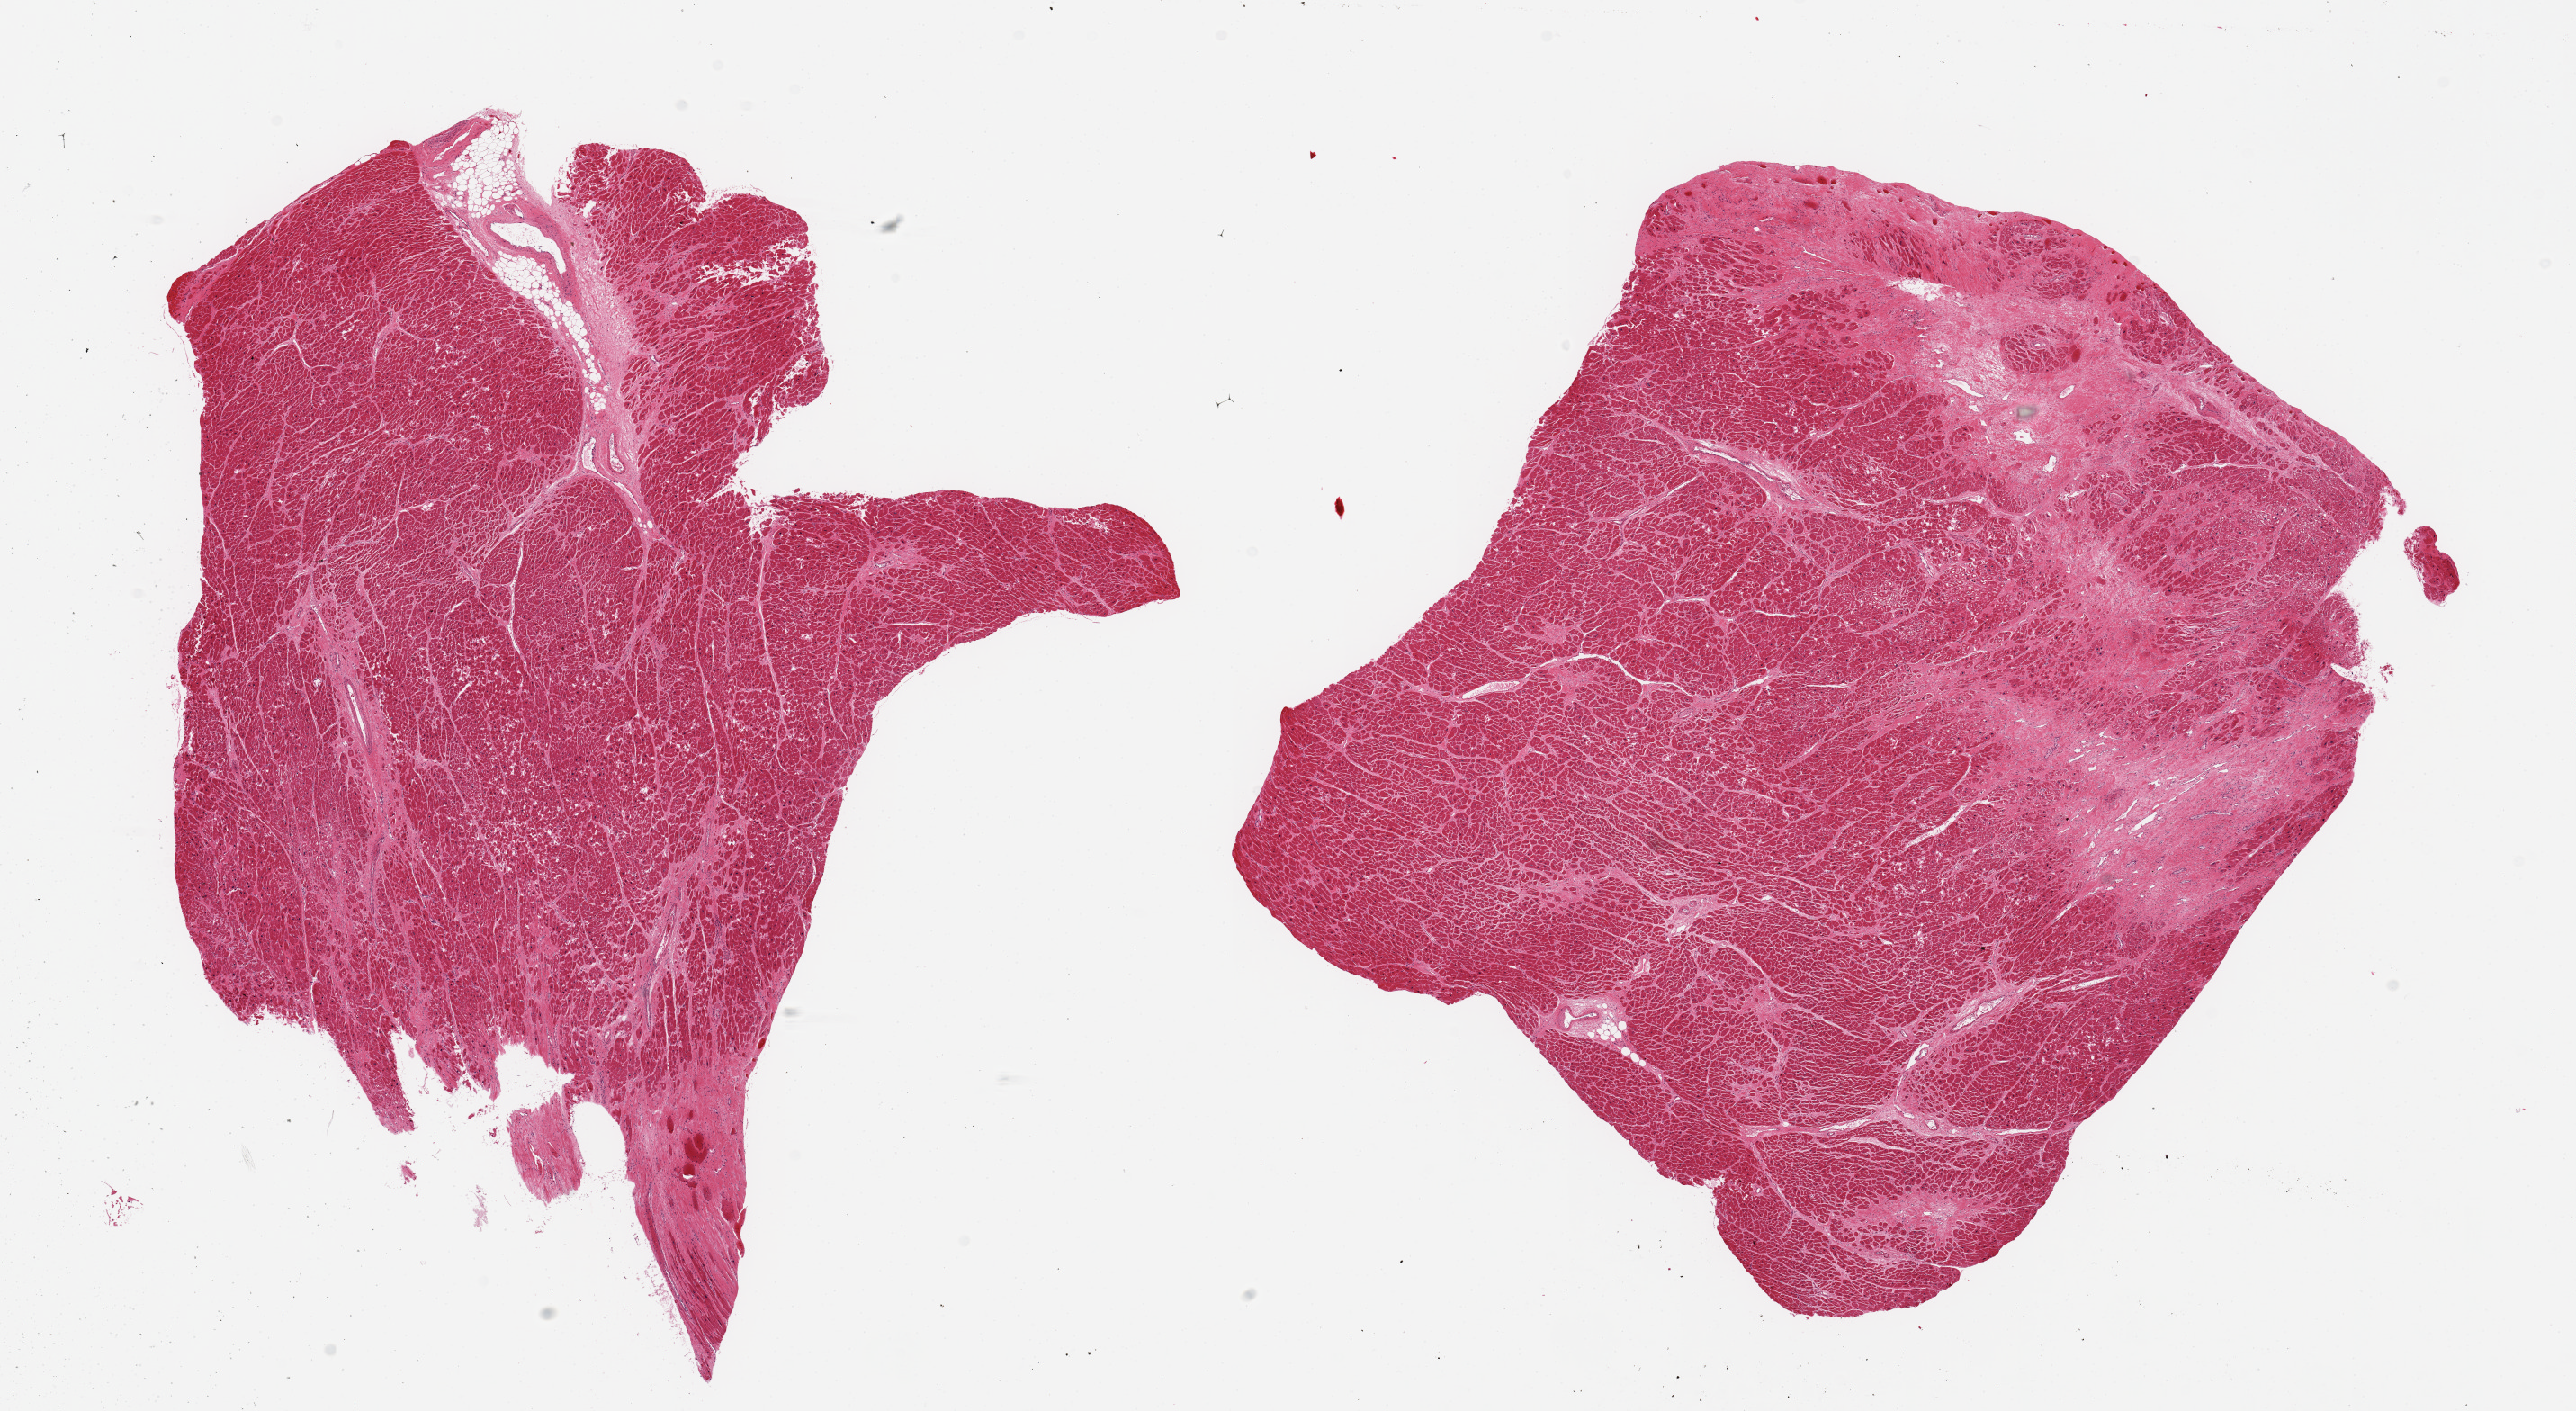
Whole-slide image, hematoxylin and eosin (H&E) stain, shown as a low-resolution overview of the whole scanned area (about 22.6 x 12.4 mm), PAXgene-fixed, paraffin-embedded tissue, sampled site (target tissue): heart, donor tissue sample. Donor: female.
- review note (as recorded): 2 pieces; interstitial fibrosis and extensive scarring; hypertrophy